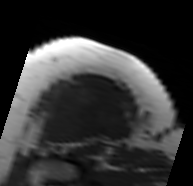
MRI of an extremity soft-tissue mass, one axial slice. Position 59 of 91 along the scan axis. MR volume resampled by the dataset authors to the PET/CT grid (not the native acquisition matrix). 3.27 mm slice thickness. 193 × 186 image matrix, field of view 188 × 182 mm. Female patient. Case-level facts recorded for this patient, not image findings: histological type: malignant solitary fibrous tumor; grade: intermediate; site of the primary tumour: right thigh.
Outlined on this slice (expert contour drawn on MRI and transferred to this co-registered scan by the dataset authors):
- gross tumour volume including surrounding oedema: box from (x=38, y=81) to (x=132, y=150) px
- gross tumour volume (mass): (x=40, y=85)–(x=128, y=148)